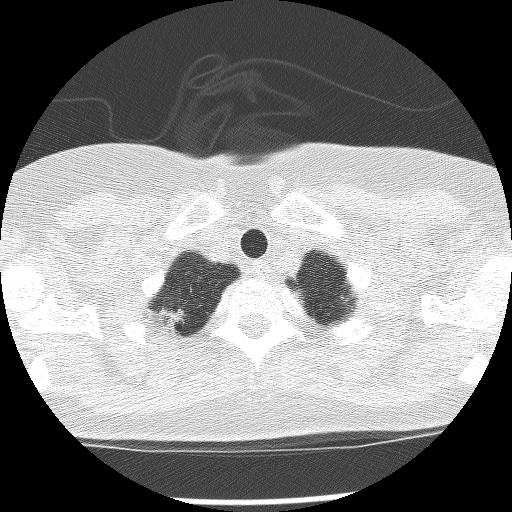
Low-dose screening chest CT, axial slice, baseline annual screen, lung window (W 1500 / L -600 HU), 2.5 mm slice thickness, lung (sharp) reconstruction kernel (BONE), 120 kVp, slice 13 of 144 in the series, 512 × 512 image matrix. Female, age 56 years at enrolment. Current smoker at enrolment.
Expert reader's lesion annotation, bounding box [x1, y1, x2, y2] px = [145, 297, 197, 341]. Screening reader's record for this exam: no non-calcified nodule ≥4 mm recorded. Lung cancer was diagnosed 729 days after this screen: large cell carcinoma, NOS, right upper lobe, poorly differentiated (G3), stage IB (AJCC 6th edition), 15 mm at pathology.